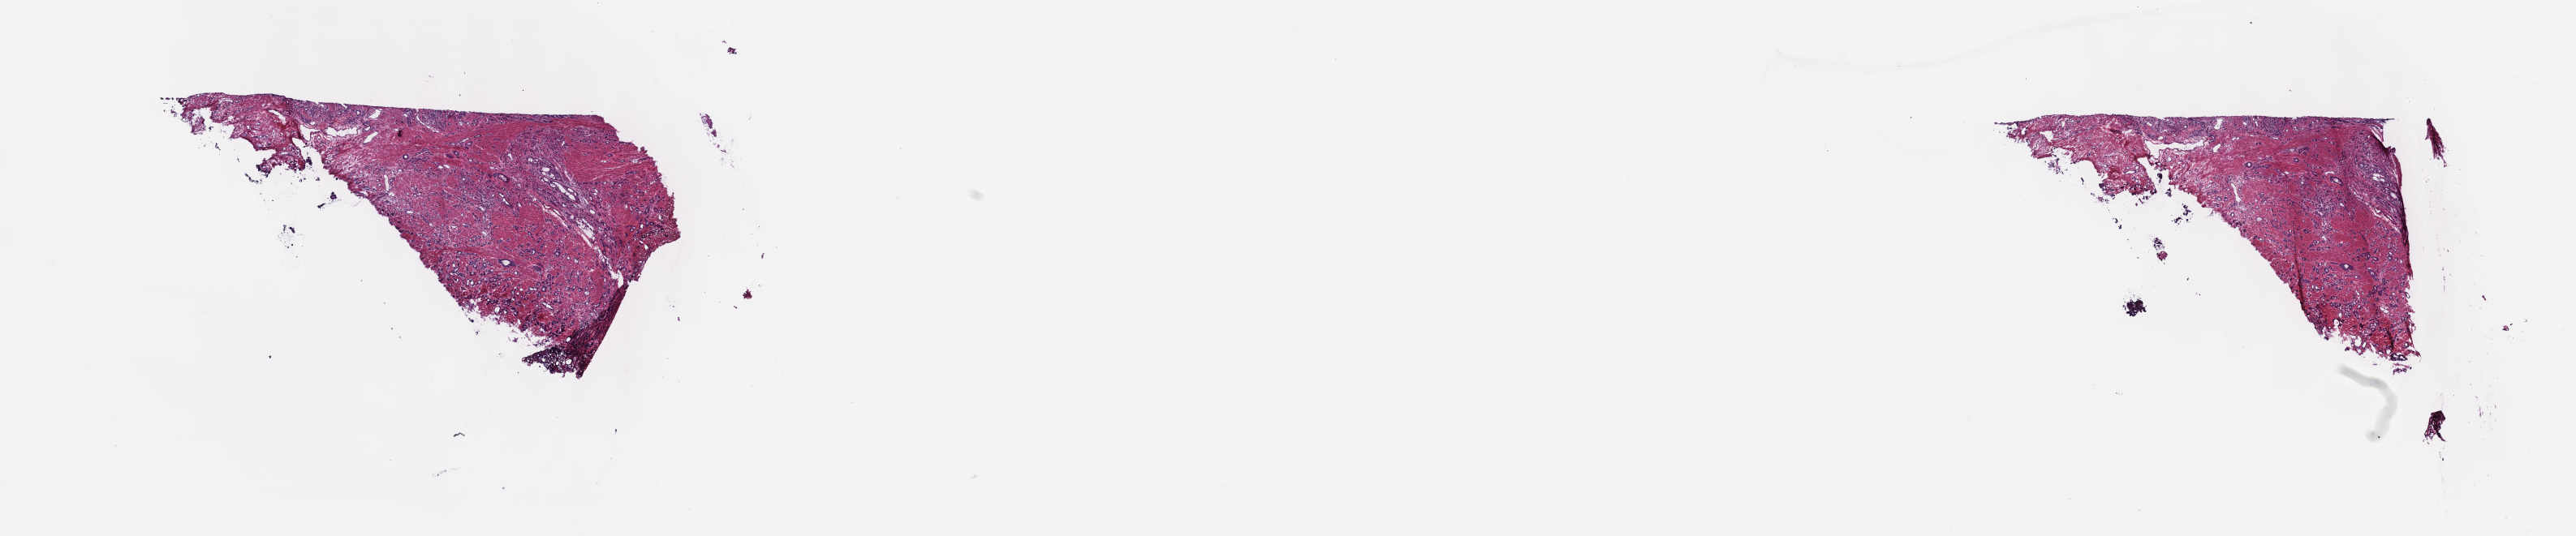
Whole-slide histology image, Hematoxylin and eosin (H&E) stained — low-resolution overview of the scanned area, about 25.7 x 5.3 mm (acquisition: 40x scan). Frozen section. Primary tumour sample from the prostate. Patient: male, age at initial diagnosis 58 years. Gleason score: 9 (4+5). Slide review estimates, as recorded: tumour cells 55%, tumour nuclei 70%, normal cells 0%, stromal cells 45%, necrosis 0%. Infiltration values recorded for this section: lymphocyte infiltration 0%, monocyte infiltration 0%, neutrophil infiltration 0%.
- histologic diagnosis: Adenocarcinoma, NOS (prostate gland)